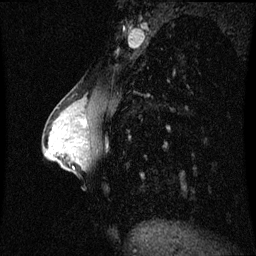
Breast MRI (dynamic contrast-enhanced), one sagittal slice; position 28 of 60 along the scan axis; dynamic contrast-enhanced series, image 2 of 3 at this slice position (ordered by acquisition); 1.5 T; TE 4.2 ms, TR 8.9 ms; 2 mm slice thickness; 256 × 256 image matrix, field of view 210 × 210 mm. Patient: female, 33 years. Case-level facts recorded for this patient, not image findings: setting: breast cancer imaged before/during neoadjuvant chemotherapy; receptor status: HER2-positive.
Outlined on this slice (semi-automatically segmented with operator editing):
- analysis volume of interest (the breast-tissue region the enhancement analysis was run in; not a lesion): bounding box [x1, y1, x2, y2] px = [66, 102, 94, 141]
- tumour enhancement mask (voxels above the 70 % enhancement threshold inside the analysis volume of interest): [84, 121, 86, 123]